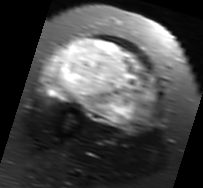
MRI of an extremity soft-tissue mass, one axial slice. Position 35 of 91 along the scan axis. T2-weighted fat-saturated. MR volume resampled by the dataset authors to the PET/CT grid (not the native acquisition matrix). 3.27 mm slice thickness. 203 × 188 image matrix, field of view 198 × 184 mm. Female patient. Case-level facts recorded for this patient, not image findings: histological type: malignant solitary fibrous tumor; grade: intermediate; site of the primary tumour: right thigh.
Structures marked on this image (expert contour drawn on MRI and transferred to this co-registered scan by the dataset authors):
- gross tumour volume including surrounding oedema: bounding box (x1, y1, x2, y2) in pixels: (40, 37, 159, 130)
- gross tumour volume (mass): (47, 37, 157, 127)